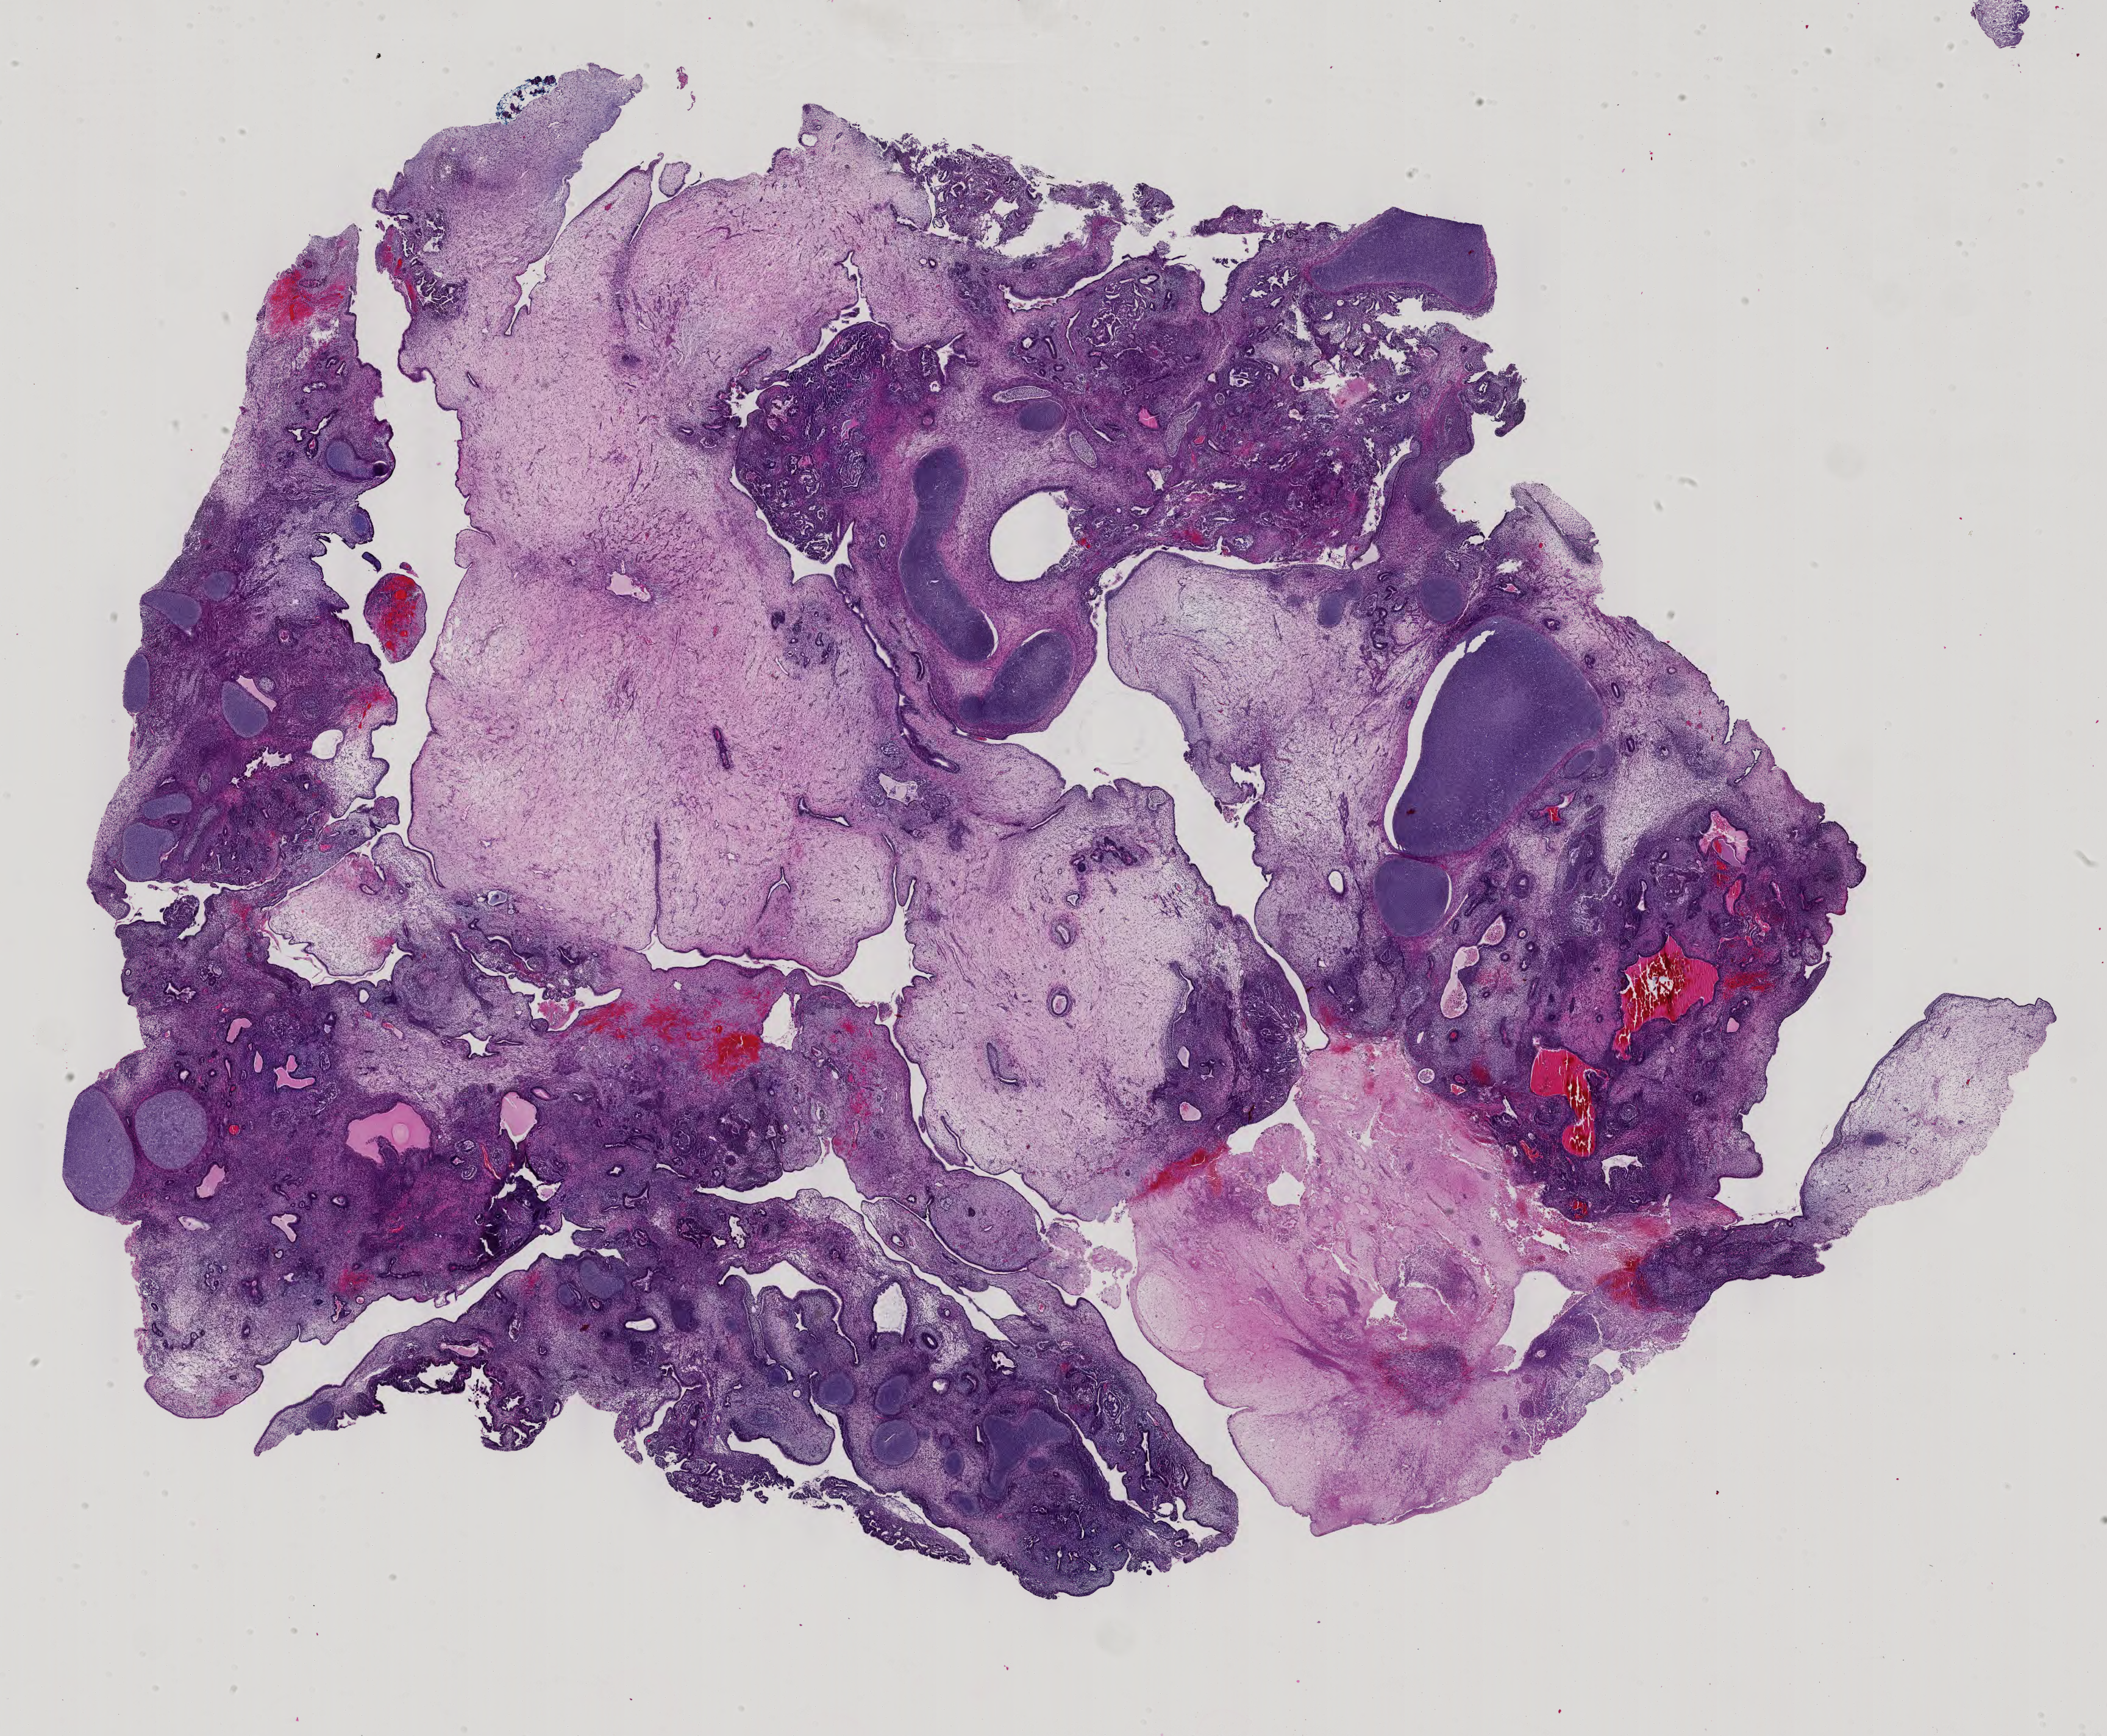
H&E whole-slide image — shown as a low-resolution overview of the whole scanned area (about 25.2 x 20.8 mm). Formalin-fixed paraffin-embedded (FFPE) diagnostic section. Sample: primary tumour, testis. Patient: male, age at initial diagnosis 23 years.
* laterality: right
* AJCC pathologic stage: I (7th edition)
* histologic diagnosis: Teratoma, malignant, NOS